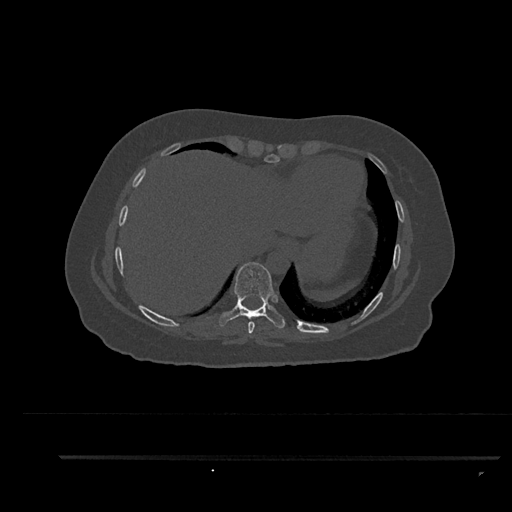
CT including the spine, one axial slice; slice 421 of 797 in the series (ordered by position); 120 kVp; bone window (W 1800 / L 400 HU); 0.5 mm slice thickness; 512 × 512 image matrix, field of view 408 × 408 mm. Patient: female, 44 years. Case-level facts recorded for this patient, not image findings: primary cancer: renal.
Structures marked on this image (semi-automatically segmented with operator editing):
- T8 vertebra: bounding box (x1, y1, x2, y2) in pixels: (248, 321, 255, 334)
- T9 vertebra: (219, 262, 286, 328)